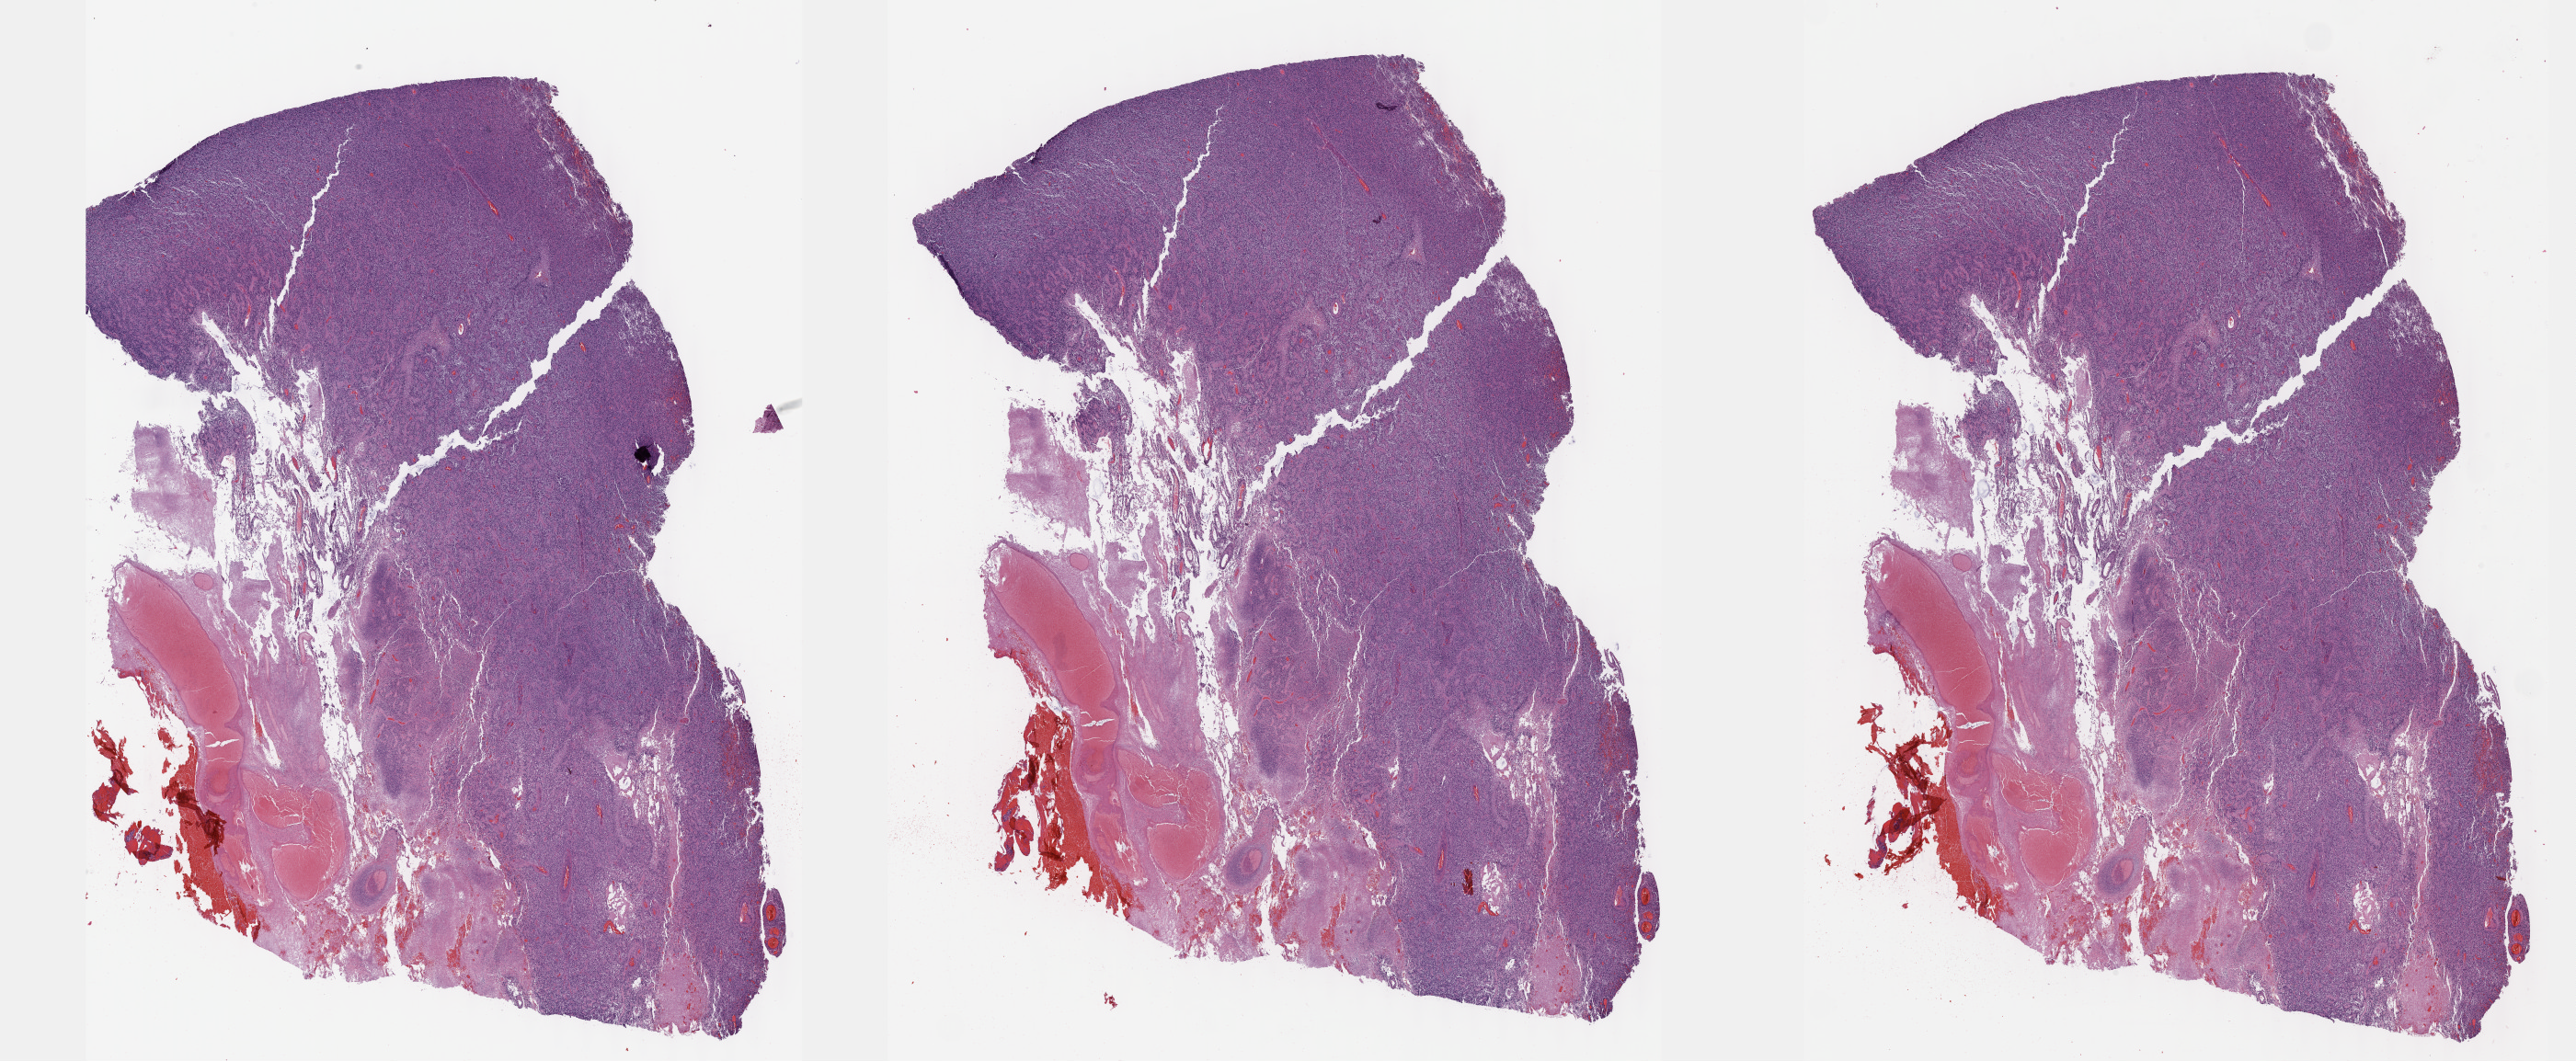
Digitized H&E tissue section (whole slide) — a low-resolution overview of the entire scanned area, about 45.3 x 18.7 mm (slide scanned at 40x). Formalin-fixed paraffin-embedded (FFPE) diagnostic section. Primary tumour sample from the brain. Male, age 40 years at initial diagnosis.
Diagnosis: Glioblastoma.